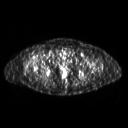
FDG PET of an extremity soft-tissue mass (from a PET/CT study), one axial slice. 3.27 mm slice thickness. 128 × 128 image matrix, field of view 500 × 500 mm. Patient: female, 57 years. Case-level facts recorded for this patient, not image findings: histological type: pleiomorphic undifferentiated sarcoma; grade: high; site of the primary tumour: right quadricep.
Outlined on this slice (expert contour drawn on MRI and transferred to this co-registered scan by the dataset authors):
- tumour plus oedema (research contour): box from (x=27, y=58) to (x=34, y=67) px